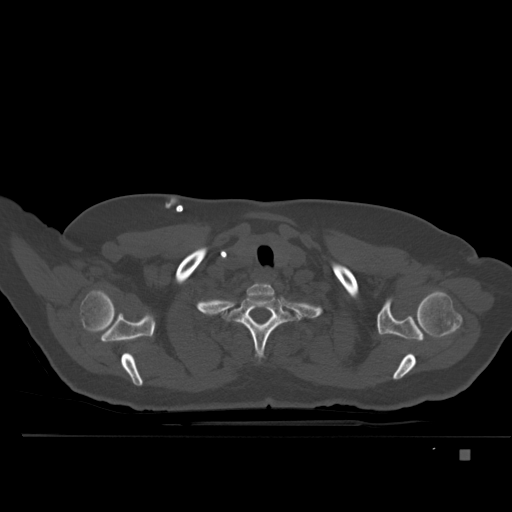
CT including the spine, one axial slice. Position 402 of 477 along the scan axis. Bone window (W 1800 / L 400 HU). 1.5 mm slice thickness. 512 × 512 image matrix, field of view 422 × 422 mm. Female patient, age 74 years. From the clinical record (not read from this slice): primary cancer: colon.
Outlined on this slice (semi-automatically segmented with operator editing):
- T1 vertebra: box from (x=233, y=293) to (x=287, y=356) px